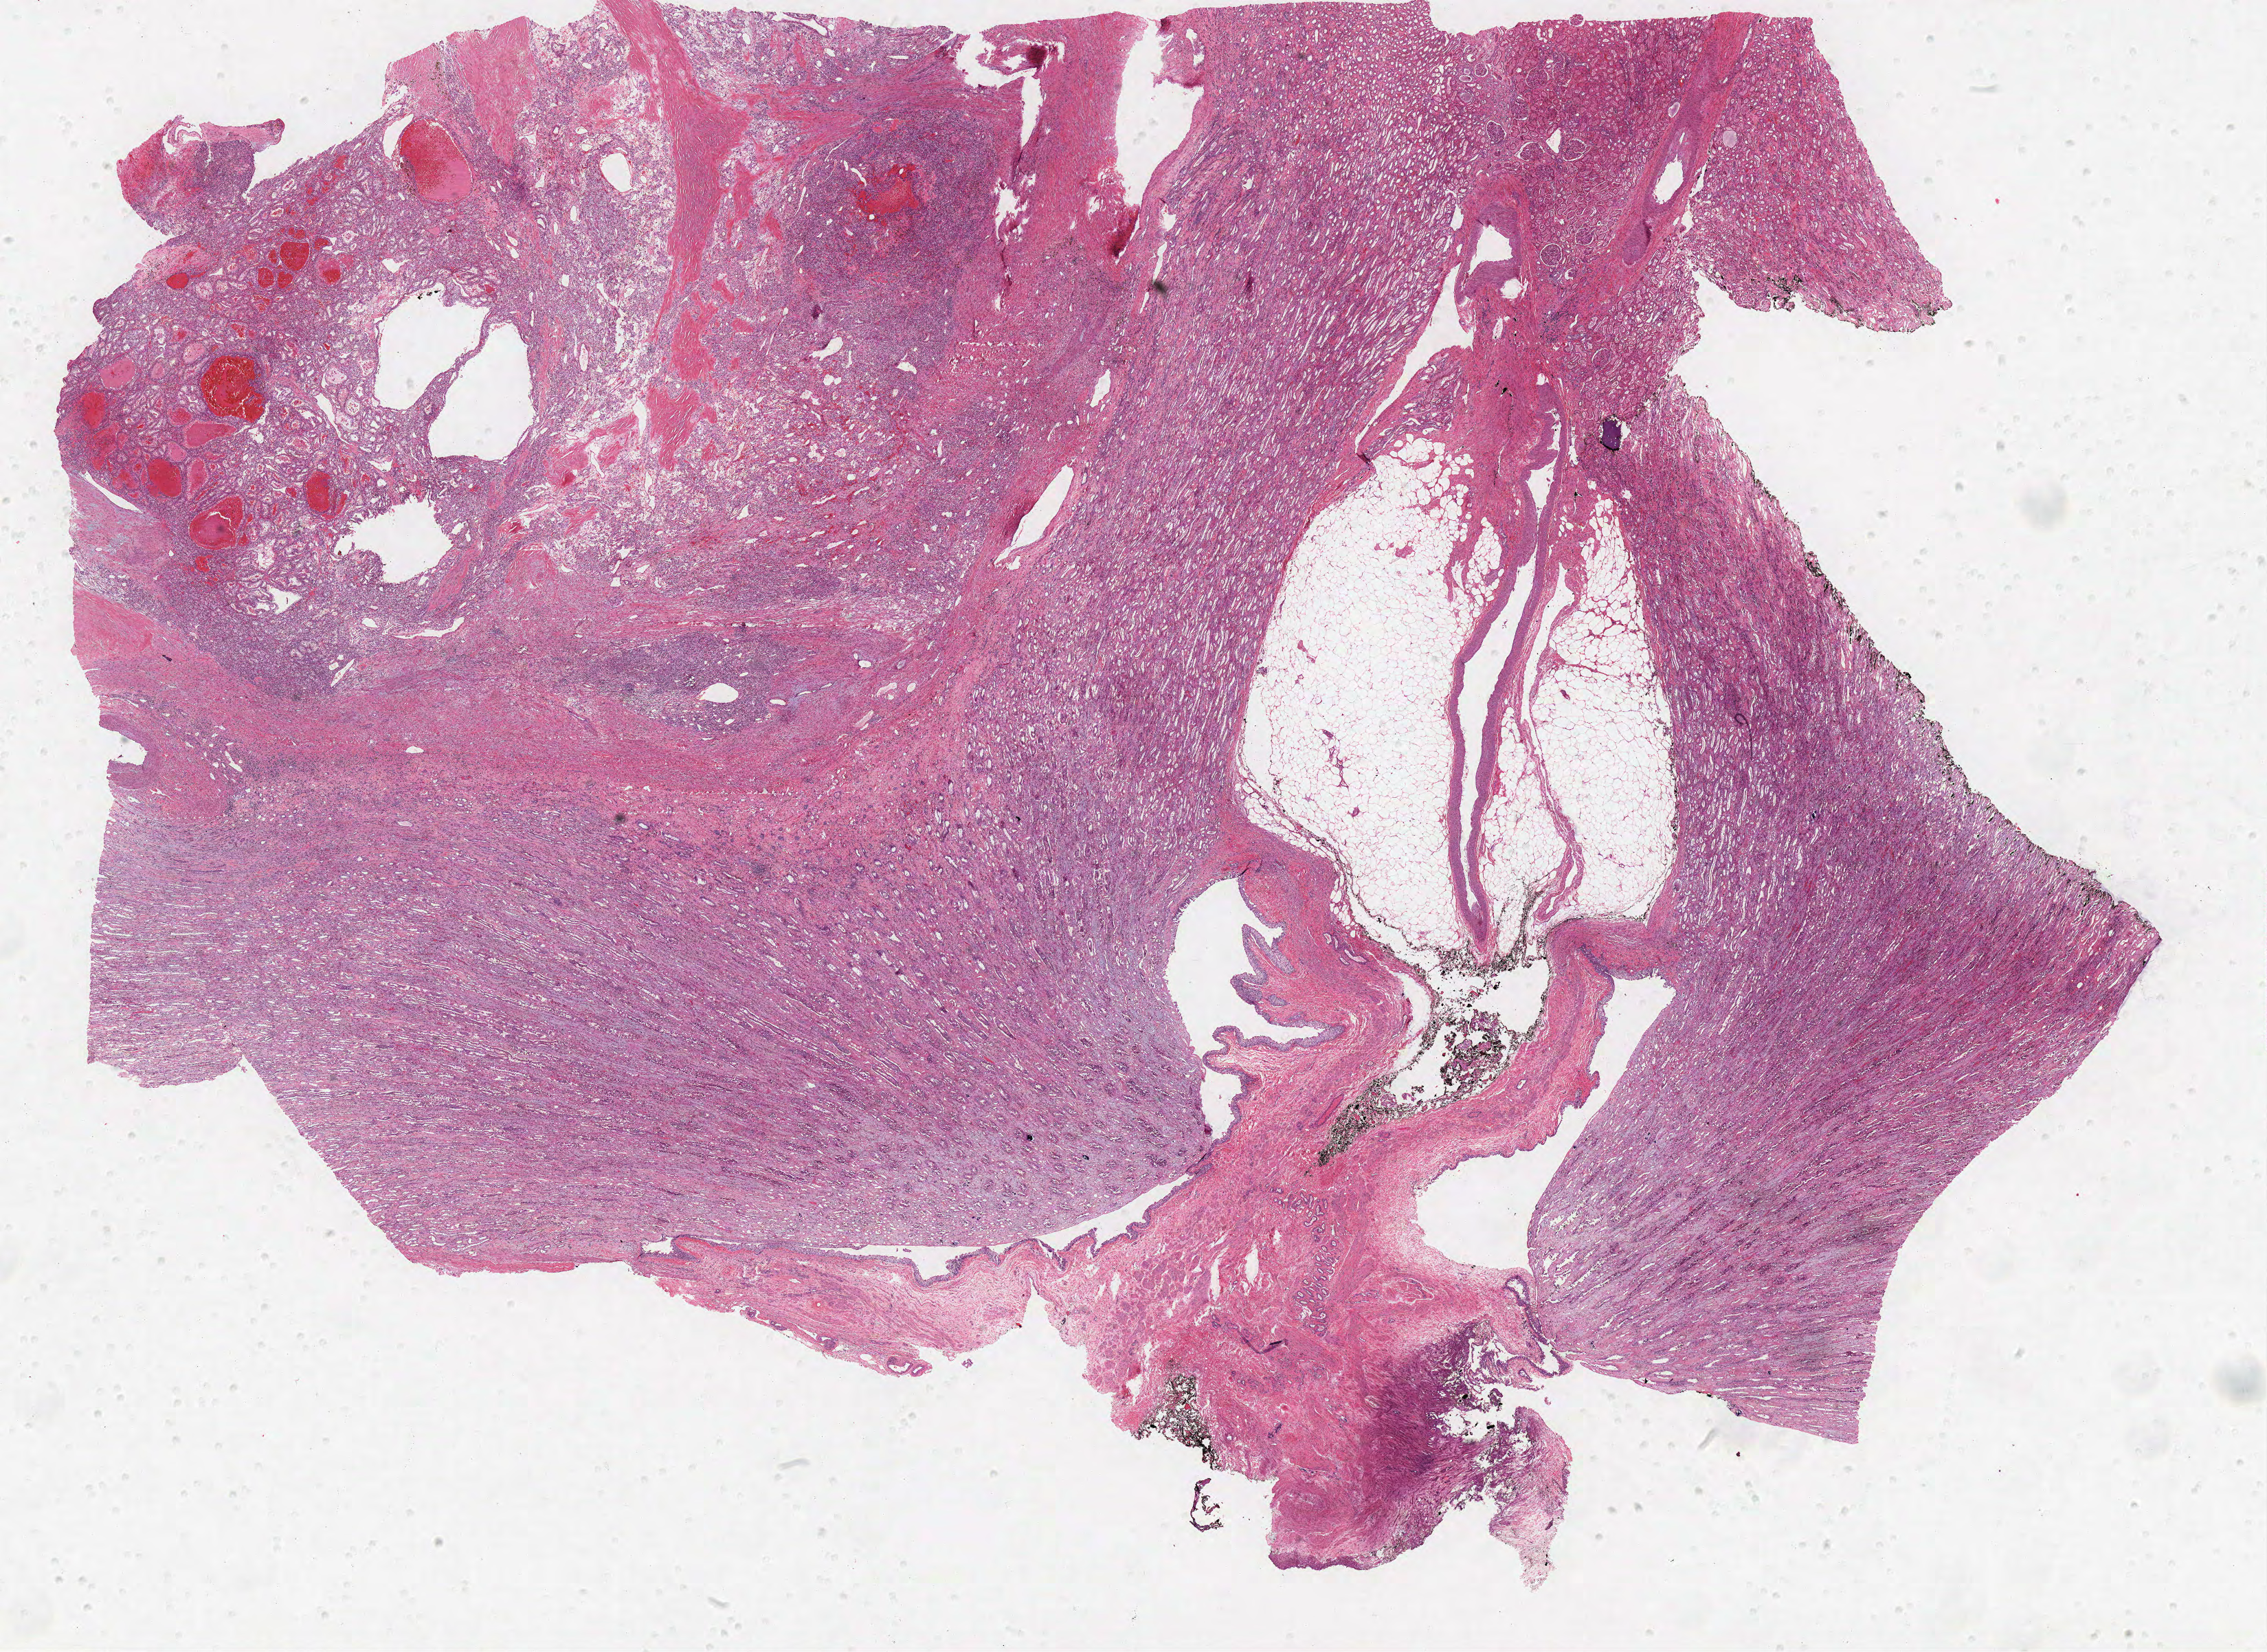
H&E whole-slide image, low-resolution overview of the scanned area, about 26.4 x 19.2 mm (acquisition: 40x scan), formalin-fixed paraffin-embedded (FFPE) diagnostic section, sample: primary tumour, kidney. Patient: male, age at initial diagnosis 49 years. Histologic grade: G3 (poorly differentiated).
• histologic diagnosis: Clear cell adenocarcinoma, NOS
• AJCC pathologic stage: I